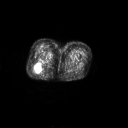
FDG PET of an extremity soft-tissue mass (from a PET/CT study), one axial slice. Position 27 of 267 along the scan axis. 3.27 mm slice thickness. 128 × 128 image matrix. Patient: female, 70 years. Case-level facts recorded for this patient, not image findings: histological type: synovial sarcoma; grade: intermediate; site of the primary tumour: right buttock.
Structures marked on this image (expert contour drawn on MRI and transferred to this co-registered scan by the dataset authors):
- gross tumour volume including surrounding oedema: bounding box <35,61,41,71> (left, top, right, bottom; pixels)
- gross tumour volume (mass): <36,64,40,68>